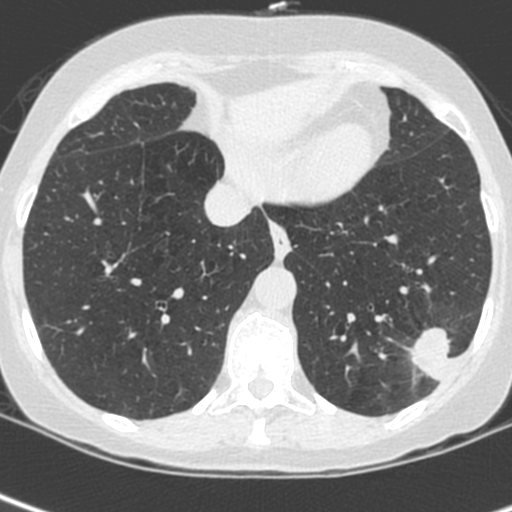
Chest CT (low-dose screening protocol), one axial image, baseline screening round, lung window (W 1500 / L -600 HU), standard (soft-tissue) reconstruction kernel (C), 512 × 512 image matrix, field of view 271 × 271 mm. Female participant, aged 56 years at enrolment. Current smoker at enrolment.
• Lesion marked by an expert reader, bounding box [x1, y1, x2, y2] px = [407, 321, 475, 389].
• Reader record for this screening exam (exam-level; its link to the box is not recorded): non-calcified nodule or mass ≥4 mm, left lower lobe, 37 × 29 mm, spiculated (stellate) margins, ground glass attenuation.
• Official screen result: positive, change unspecified: nodule(s) >= 4 mm or enlarging nodule(s), mass(es), or other non-specific abnormalities suspicious for lung cancer.
• Participant outcome: lung cancer diagnosed 91 days after this screen — squamous cell carcinoma, NOS, left lower lobe, poorly differentiated (G3), stage IIIA (AJCC 6th edition), 35 mm at pathology.